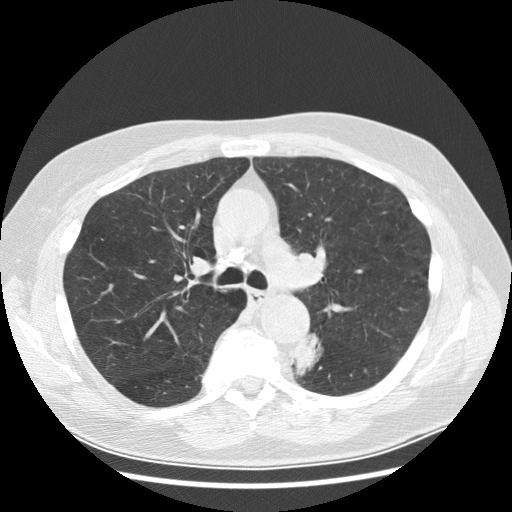
Low-dose screening chest CT, one axial slice. Reconstruction kernel STANDARD. 120 kVp. Lung window (W 1500 / L -600 HU). 2.5 mm slice thickness. 512 × 512 image matrix, field of view 370 × 370 mm.
Outlined on this slice (expert manual segmentation):
- lesion 1 (tumor, lower lobe of left lung): bounding box [x1, y1, x2, y2] px = [294, 333, 322, 377]